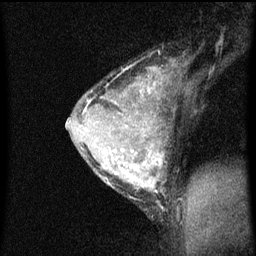
Breast MRI (dynamic contrast-enhanced), one sagittal slice. Slice 44 of 60 in the series (ordered by position). Dynamic contrast-enhanced series, image 2 of 3 at this slice position (ordered by acquisition). 1.5 T. TE 4.2 ms, TR 8 ms. 2 mm slice thickness. 256 × 256 image matrix. Female patient, age 33 years.
Outlined on this slice (semi-automatic segmentation, software-assisted and operator-edited):
- analysis volume of interest (the breast-tissue region the enhancement analysis was run in; not a lesion): box from (x=66, y=64) to (x=185, y=215) px
- tumour enhancement mask (voxels above the 70 % enhancement threshold inside the analysis volume of interest): (x=83, y=68)–(x=165, y=209)